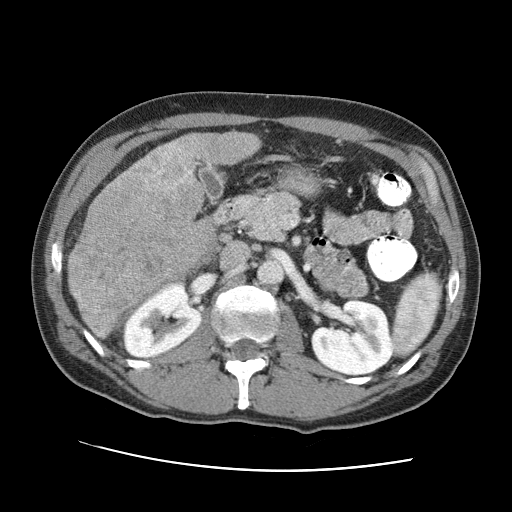
Contrast-enhanced abdominal CT (liver protocol), one axial slice. Slice 32 of 95 in the series (ordered by position). Reconstruction kernel STANDARD. One of 2 acquisitions stored at this slice position. Soft-tissue window (W 400 / L 40 HU). 2.5 mm slice thickness. 512 × 512 image matrix, field of view 360 × 360 mm. Case-level facts recorded for this patient, not image findings: diagnosis: hepatocellular carcinoma (patient treated with transarterial chemoembolisation; whether this scan precedes or follows treatment is not stated here); TNM stage (as recorded): Stage-IVA; Child-Pugh class: A; tumour nodularity: multinodular.
Annotated regions visible in this slice (semi-automatic segmentation, software-assisted and operator-edited):
- liver parenchyma outside the tumour (the mass and vessels are separate outlines, so this box may not span the whole liver): bounding box (x1, y1, x2, y2) in pixels: (68, 132, 260, 330)
- mass: (67, 146, 215, 340)
- liver vessels: (169, 143, 224, 213)